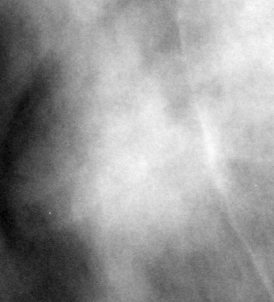
Cropped region of a digitized screen-film mammogram centred on a radiologist-marked abnormality; right breast; CC view; BI-RADS breast density category 2 (scale 1–4).
Marked abnormality: mass, shape oval, margins microlobulated; BI-RADS assessment category 4; pathology (as recorded): benign.